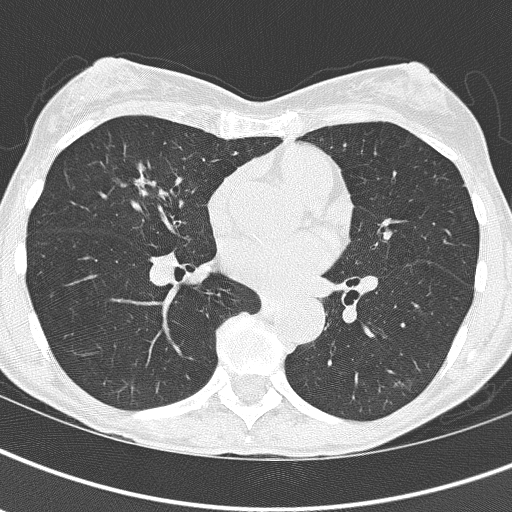
Chest CT (low-dose screening protocol), one axial image; first (baseline) screen; lung window (W 1500 / L -600 HU); 2 mm slice thickness; 512 × 512 image matrix, field of view 290 × 290 mm. Female participant, aged 67 years at enrolment. Current smoker at enrolment.
Expert reader's lesion annotation, bounding box (x1, y1, x2, y2) in pixels: (92, 142, 175, 222). No non-calcified nodule or mass ≥4 mm was recorded by the screening reader at this exam. Later outcome: lung cancer diagnosed 832 days after this screen — bronchiolo-alveolar adenocarcinoma, NOS, right middle lobe, well differentiated (G1), stage IA (AJCC 6th edition), 25 mm at pathology.